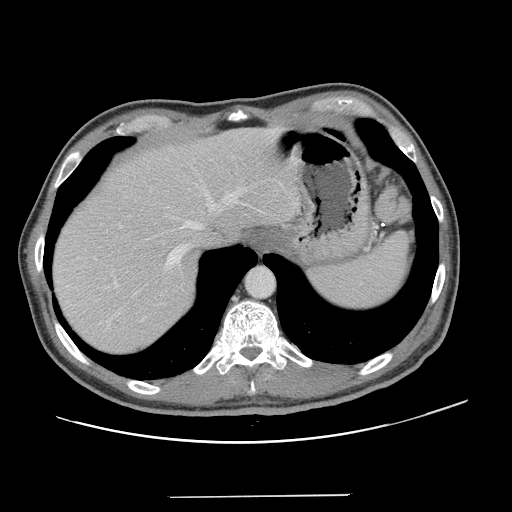
Contrast-enhanced abdominal CT, one axial slice; slice 108 of 131 in the series (ordered by position); soft-tissue window (W 400 / L 40 HU); 2.5 mm slice thickness; 512 × 512 image matrix, field of view 403 × 403 mm. Male patient, age 60 years. From the clinical record (not read from this slice): diagnosis: colorectal cancer liver metastases, imaged before liver resection; multiple liver metastases: no; largest metastasis: 2.5 cm; disease in both lobes: no.
Outlined on this slice (outlined manually by an expert reader):
- hepatic veins: bounding box (x1, y1, x2, y2) in pixels: (164, 180, 245, 272)
- liver: (53, 128, 298, 356)
- planned liver remnant (the part of the liver to remain after resection): (53, 128, 299, 346)